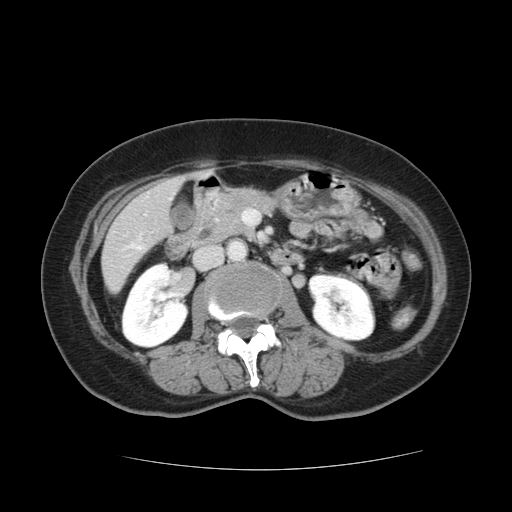
Contrast-enhanced abdominal CT, one axial slice; slice 41 of 128 in the series (ordered by position); 120 kVp; intravenous contrast given; soft-tissue window (W 400 / L 40 HU); 2.5 mm slice thickness; 512 × 512 image matrix, field of view 366 × 366 mm. Female patient, age 67 years. Case-level facts recorded for this patient, not image findings: diagnosis: colorectal cancer liver metastases, imaged before liver resection; multiple liver metastases: yes; largest metastasis: 3 cm; disease in both lobes: yes.
Structures marked on this image (manually delineated by an expert):
- hepatic veins: bounding box (x1, y1, x2, y2) in pixels: (137, 246, 141, 249)
- liver: (102, 176, 182, 292)
- planned liver remnant (the part of the liver to remain after resection): (102, 220, 155, 291)